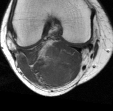
MRI of an extremity soft-tissue mass, one axial slice. Position 14 of 45 along the scan axis. MR volume resampled by the dataset authors to the PET/CT grid (not the native acquisition matrix). 3.27 mm slice thickness. 113 × 111 image matrix, field of view 110 × 108 mm. Female patient. Case-level facts recorded for this patient, not image findings: histological type: liposarcoma; site of the primary tumour: right thigh.
Outlined on this slice (expert contour drawn on MRI and transferred to this co-registered scan by the dataset authors):
- gross tumour volume (mass): box from (x=30, y=43) to (x=73, y=86) px